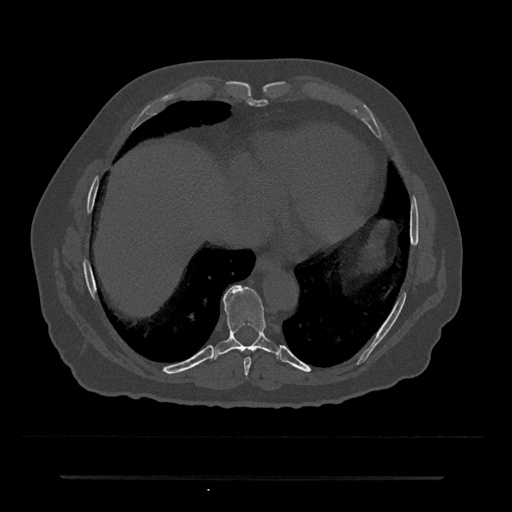
CT including the spine, one axial slice. Position 288 of 797 along the scan axis. Reconstruction kernel Br40s/3. Bone window (W 1800 / L 400 HU). 512 × 512 image matrix, field of view 437 × 437 mm. Patient: male, 69 years. From the clinical record (not read from this slice): primary cancer: prostate.
Annotated regions visible in this slice (semi-automatically segmented with operator editing):
- T8 vertebra: bounding box [x1, y1, x2, y2] px = [244, 357, 252, 376]
- T9 vertebra: [214, 285, 279, 357]